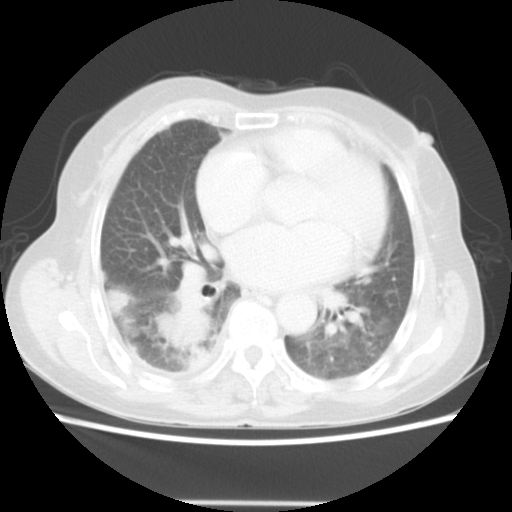
Chest CT, one axial slice. Position 24 of 52 along the scan axis. 140 kVp. Lung window (W 1500 / L -600 HU). 5 mm slice thickness. 512 × 512 image matrix, field of view 337 × 337 mm. Patient: female, 67 years. Case-level facts recorded for this patient, not image findings: clinical TNM (as recorded): T3 N1 M1.
Annotated regions visible in this slice (bounding box drawn by a radiologist):
- lung tumour (recorded histology: adenocarcinoma): bounding box <157,293,216,359> (left, top, right, bottom; pixels)